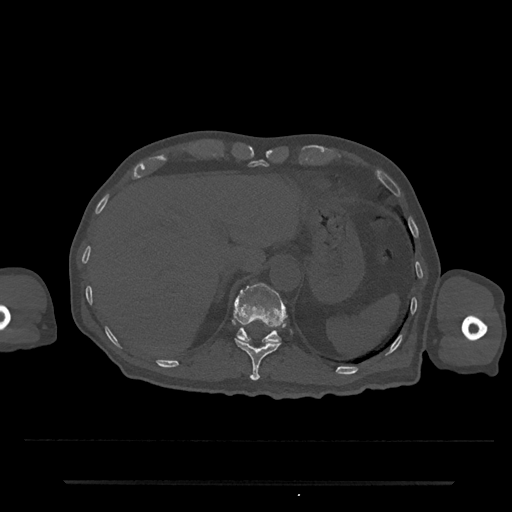
CT including the spine, one axial slice; slice 231 of 797 in the series (ordered by position); reconstruction kernel Br40s/3; 120 kVp; bone window (W 1800 / L 400 HU); 0.5 mm slice thickness; 512 × 512 image matrix, field of view 427 × 427 mm. Male patient, age 74 years. Case-level facts recorded for this patient, not image findings: primary cancer: prostate.
Annotated regions visible in this slice (semi-automatic segmentation, software-assisted and operator-edited):
- T11 vertebra: bounding box <235,338,281,381> (left, top, right, bottom; pixels)
- T12 vertebra: <234,283,285,344>